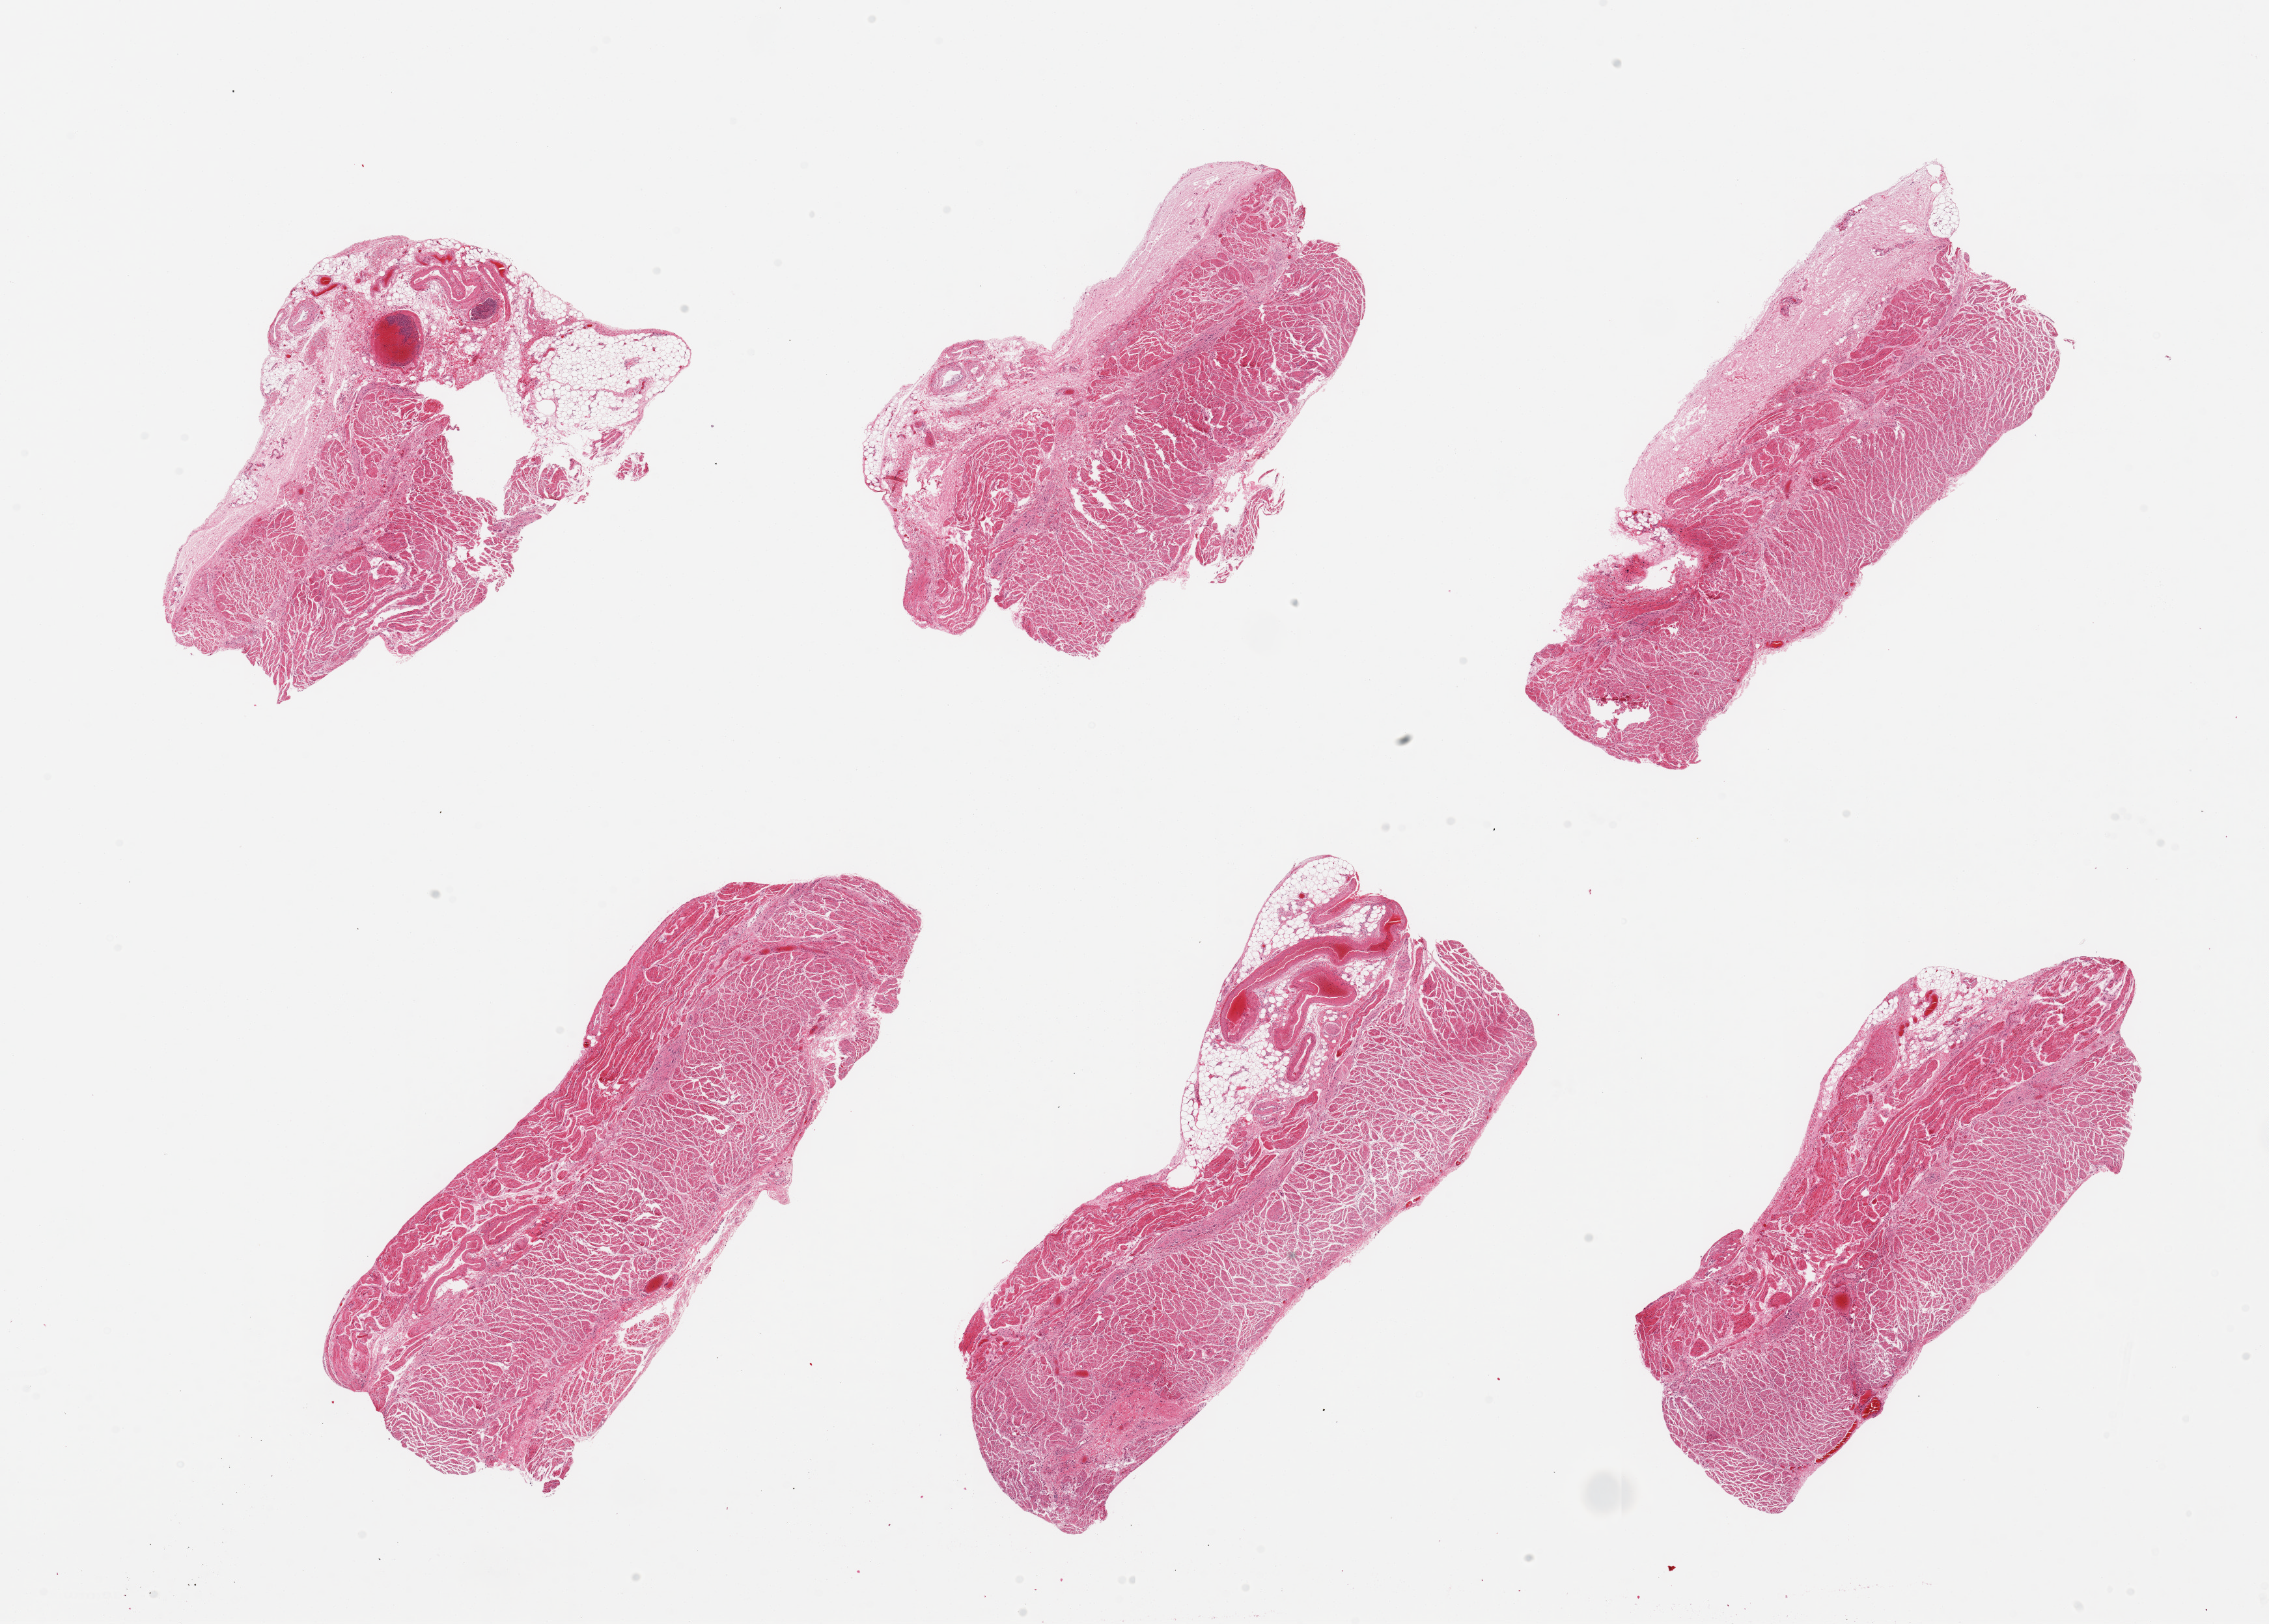
Whole-slide image, haematoxylin and eosin stain — whole scanned area (about 27.6 x 19.7 mm) shown as a low-resolution overview; PAXgene-fixed paraffin-embedded (PFPE) section; section of gastroesophageal junction (target tissue); tissue donor sample. Donor: male.
Pathologist's review note for this sample: 6 pieces; 4 of 6 pieces have moderate amount of external fibrofatty stroma.